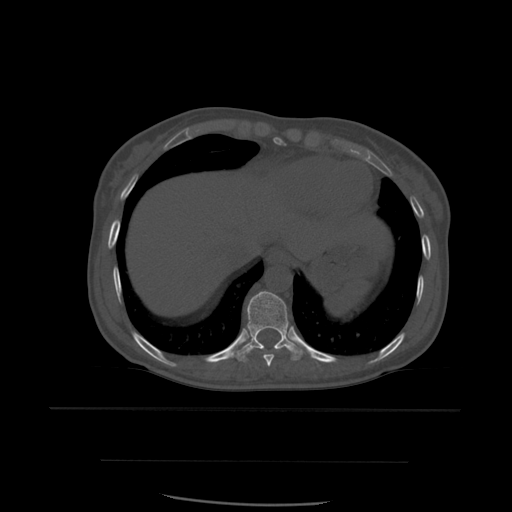
CT including the spine, one axial slice. Slice 323 of 574 in the series (ordered by position). Bone window (W 1800 / L 400 HU). 512 × 512 image matrix, field of view 392 × 392 mm. Patient age 48 years. Case-level facts recorded for this patient, not image findings: primary cancer: lung; vertebrae with lytic lesions (as recorded): T11.
Outlined on this slice (semi-automatic segmentation, software-assisted and operator-edited):
- T10 vertebra: bounding box [x1, y1, x2, y2] px = [234, 291, 306, 362]
- T9 vertebra: [249, 347, 290, 367]